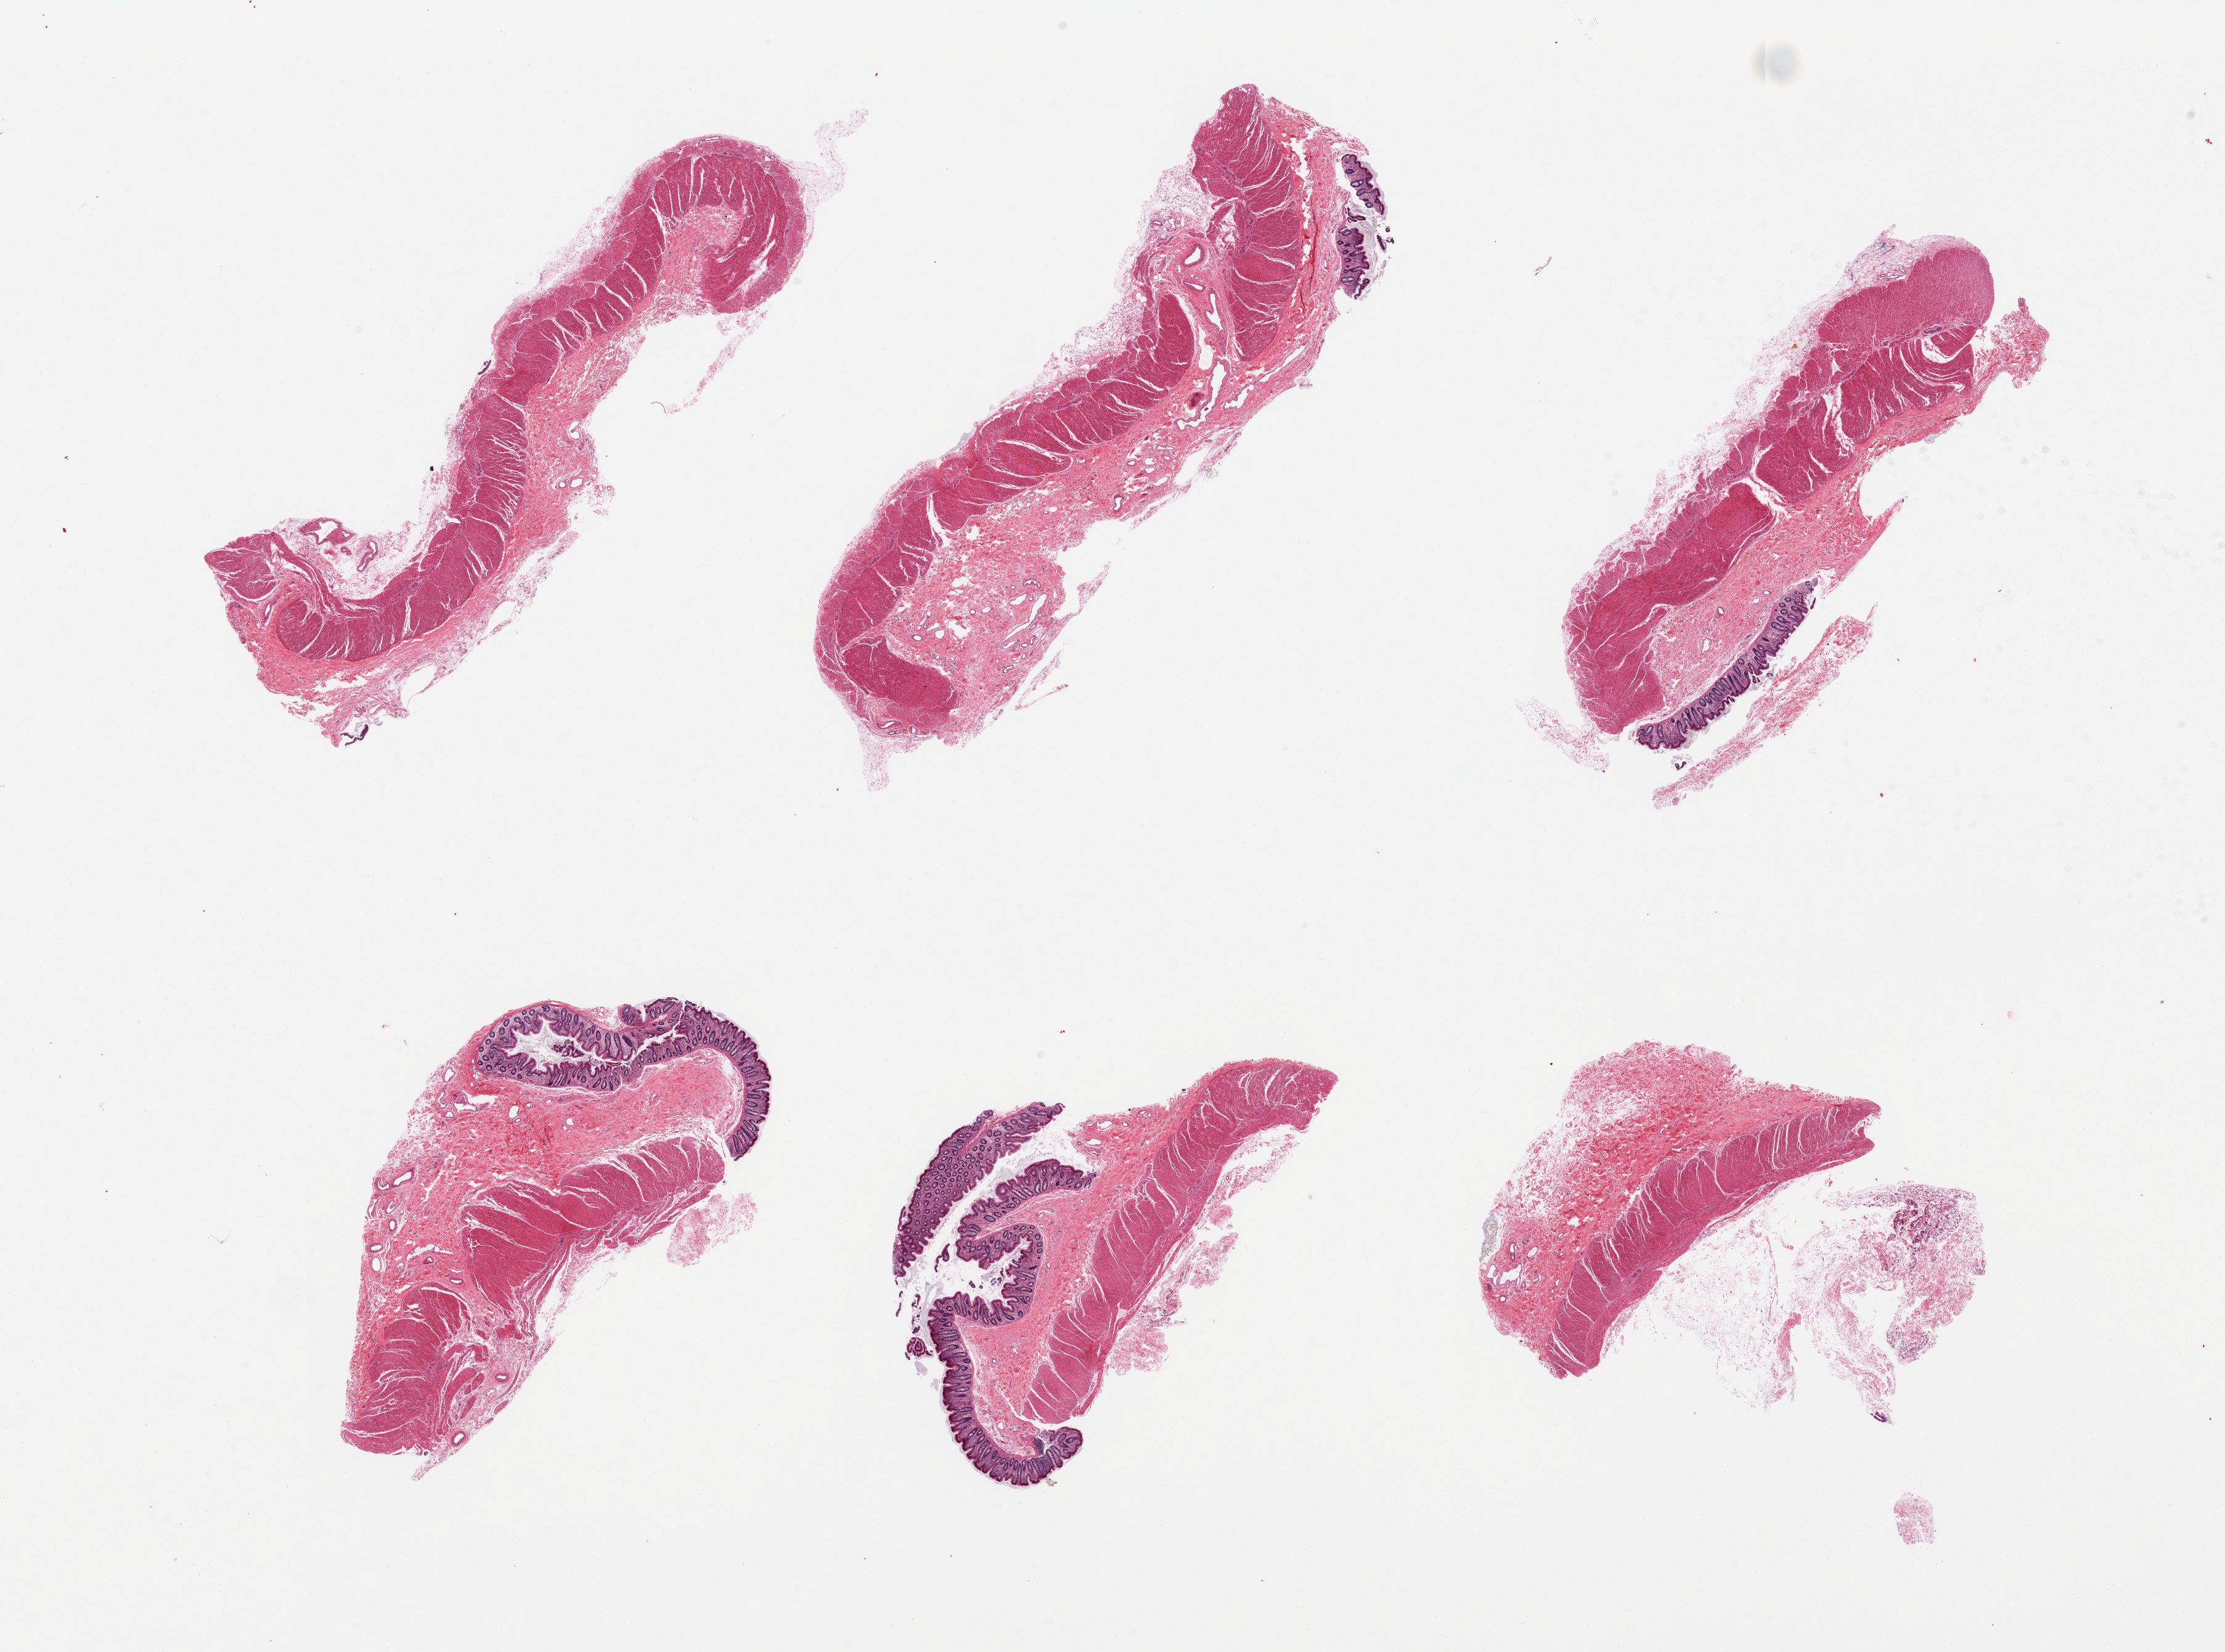
Whole-slide image, hematoxylin and eosin (H&E) stain — low-resolution overview of the scanned area, about 28.5 x 21.2 mm. PAXgene-fixed paraffin-embedded (PFPE) section. Sampled site (target tissue): transverse colon. Donor tissue sample. Male donor.
Reviewer comment on this tissue sample: 6 pieces, 2 without mucosa.